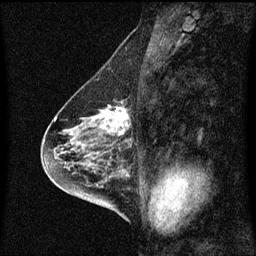
Breast MRI (dynamic contrast-enhanced), one sagittal slice. Slice 31 of 60 in the series (ordered by position). Dynamic contrast-enhanced series, image 2 of 3 at this slice position (ordered by acquisition). 1.5 T. TE 4.2 ms, TR 8.4 ms. 2 mm slice thickness. 256 × 256 image matrix, field of view 200 × 200 mm. Patient: female, 58 years.
Structures marked on this image (semi-automatic segmentation, software-assisted and operator-edited):
- analysis volume of interest (the breast-tissue region the enhancement analysis was run in; not a lesion): bounding box (x1, y1, x2, y2) in pixels: (86, 102, 132, 143)
- tumour enhancement mask (voxels above the 70 % enhancement threshold inside the analysis volume of interest): (91, 102, 131, 137)